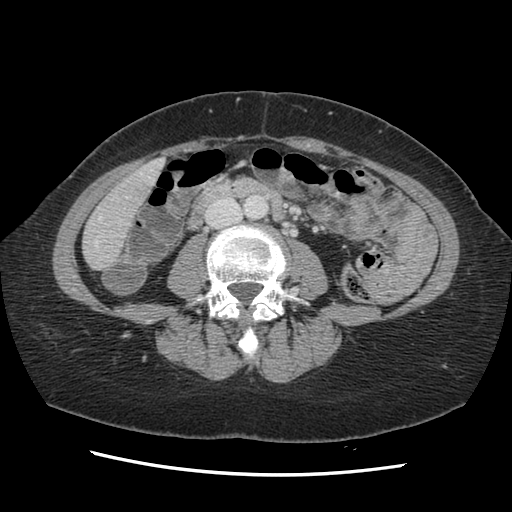
Contrast-enhanced abdominal CT, one axial slice. Slice 29 of 141 in the series (ordered by position). Soft-tissue window (W 400 / L 40 HU). 2.5 mm slice thickness. 512 × 512 image matrix, field of view 330 × 330 mm. Female patient, age 61 years. Case-level facts recorded for this patient, not image findings: diagnosis: colorectal cancer liver metastases, imaged before liver resection; multiple liver metastases: no; largest metastasis: 2.4 cm.
Outlined on this slice (manually delineated by an expert):
- hepatic veins: bounding box <95,173,154,248> (left, top, right, bottom; pixels)
- liver: <84,161,163,270>
- planned liver remnant (the part of the liver to remain after resection): <84,161,163,270>